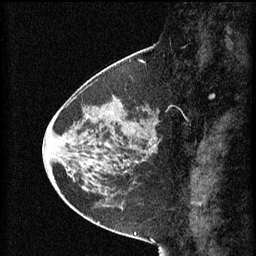
Breast MRI (dynamic contrast-enhanced), one sagittal slice. Position 27 of 60 along the scan axis. 3 images stored at this slice position (order not interpretable as contrast timing). 1.5 T. TE 4.2 ms, TR 8.2 ms. 2 mm slice thickness. 256 × 256 image matrix, field of view 200 × 200 mm. Patient: female, 45 years.
Annotated regions visible in this slice (semi-automatically segmented with operator editing):
- analysis volume of interest (the breast-tissue region the enhancement analysis was run in; not a lesion): box from (x=80, y=102) to (x=157, y=171) px
- tumour enhancement mask (voxels above the 70 % enhancement threshold inside the analysis volume of interest): (x=87, y=160)–(x=93, y=165)